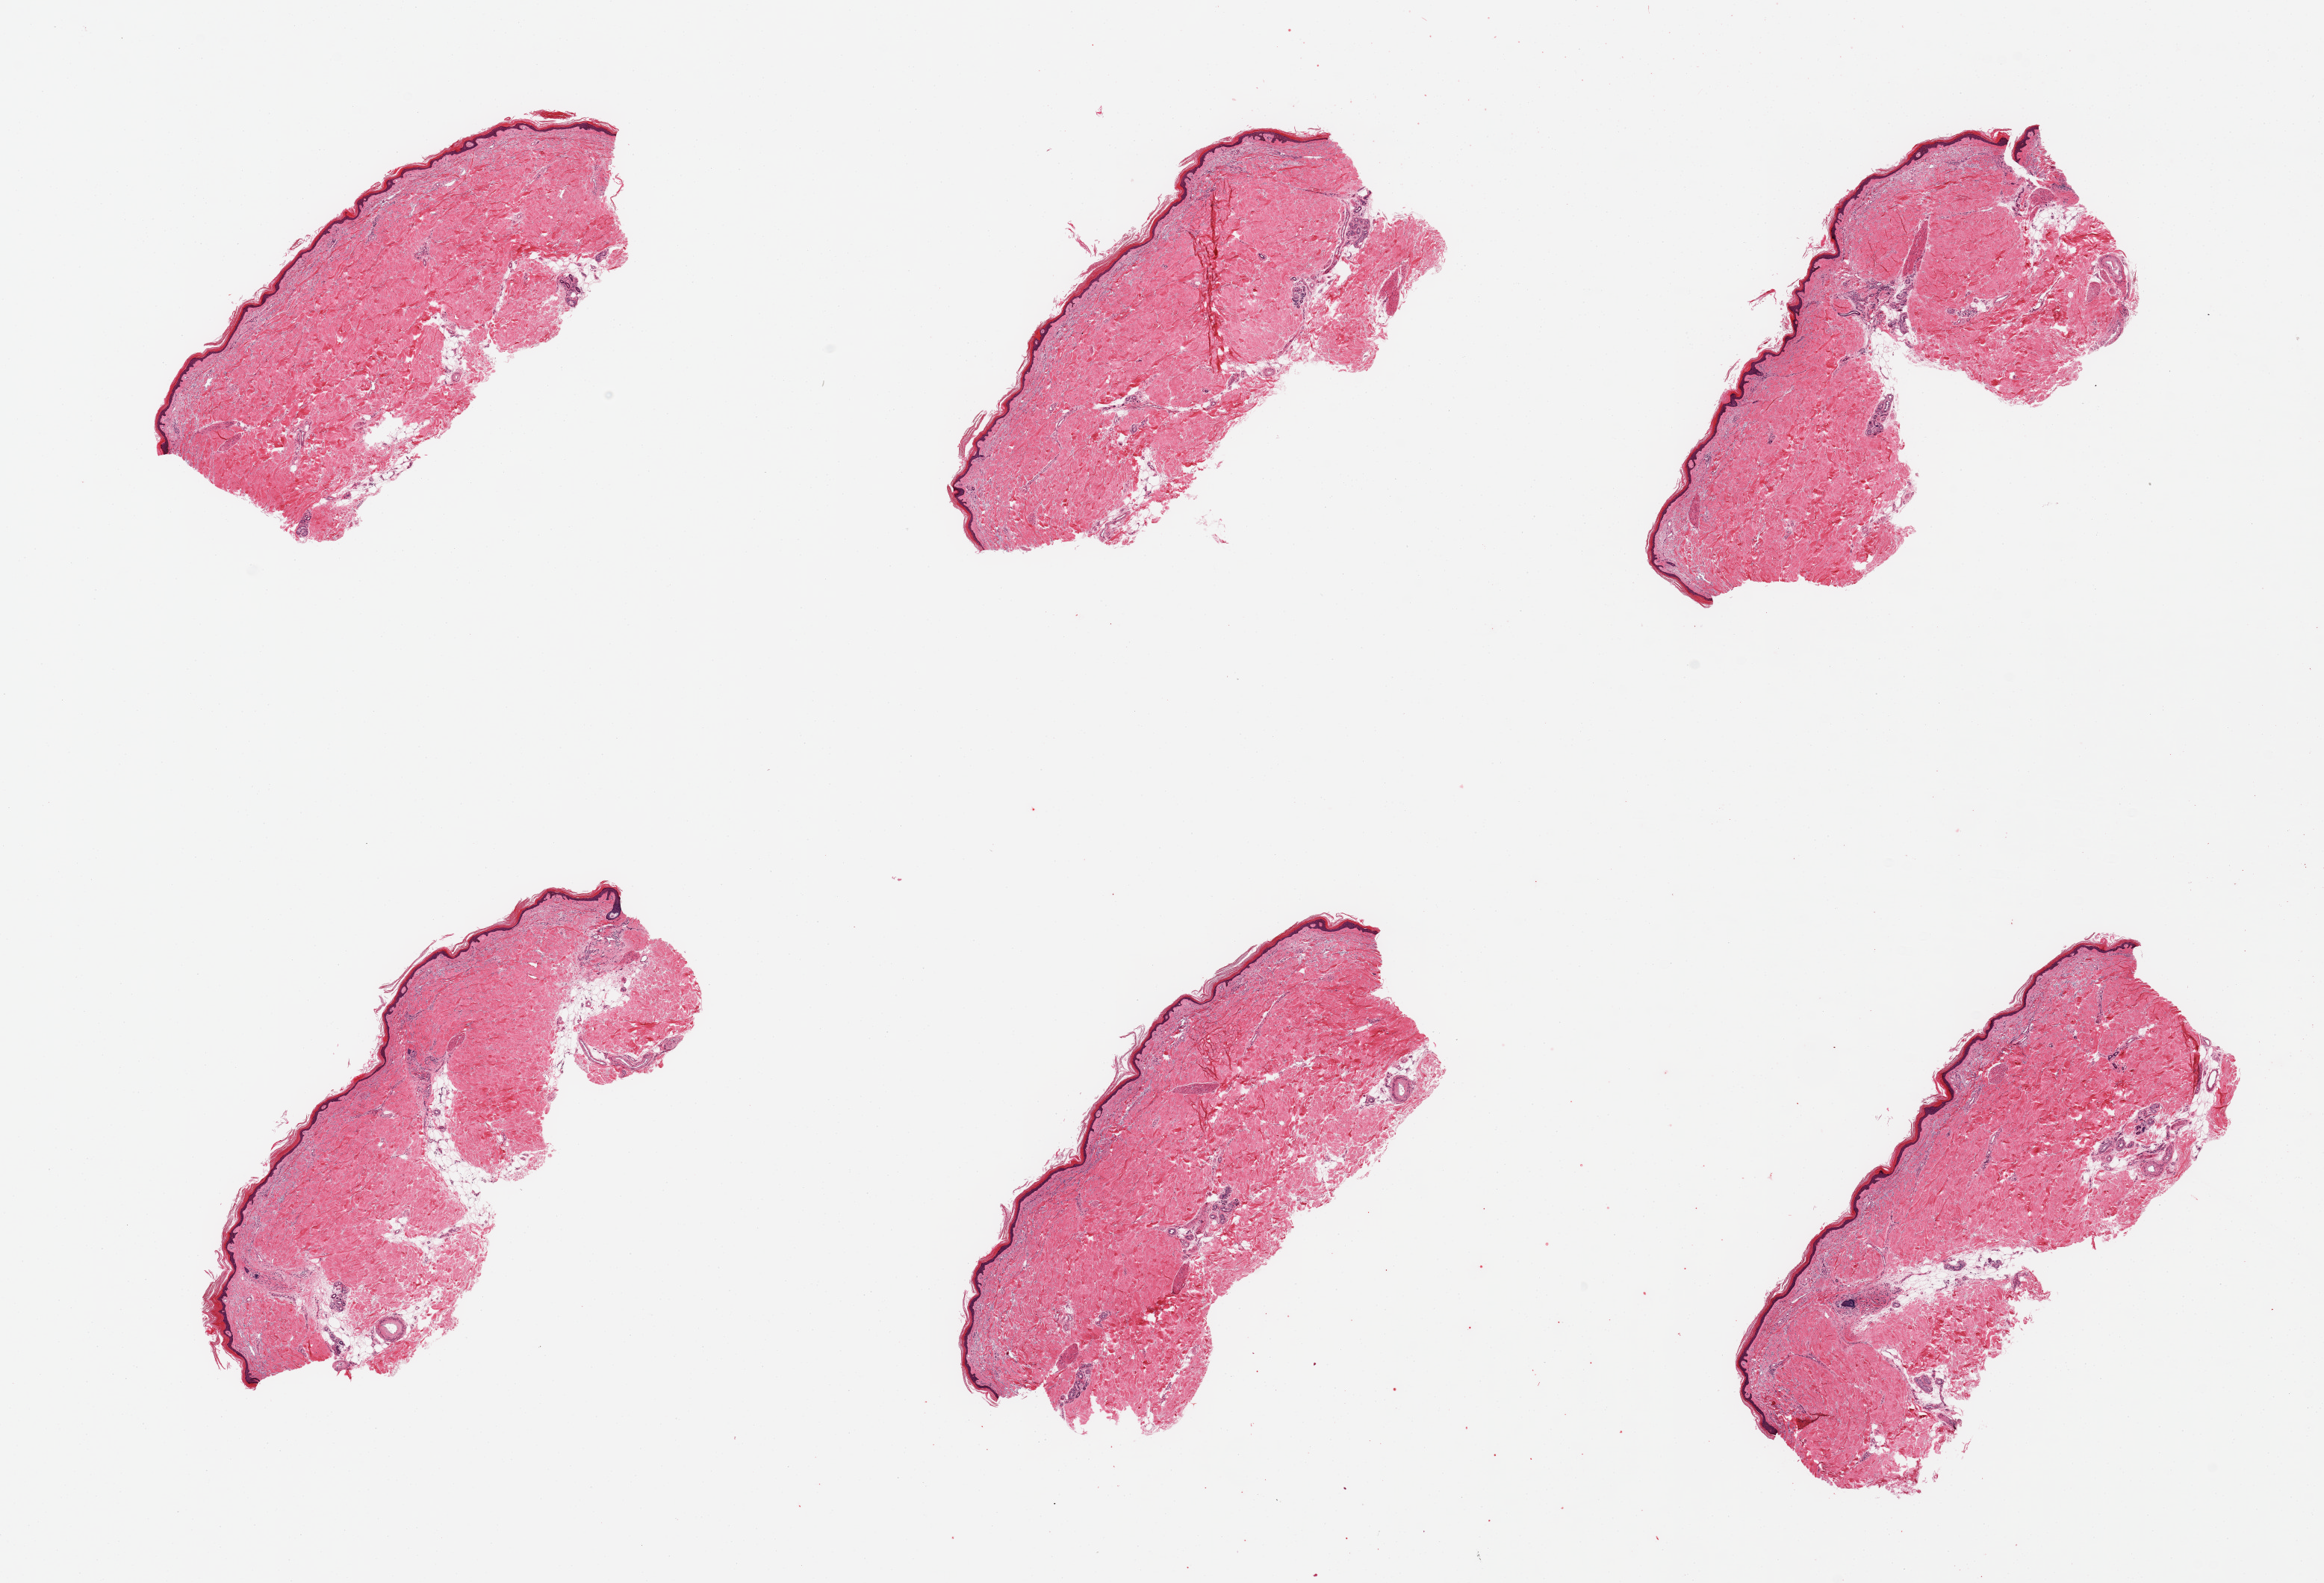
H&E whole-slide image, whole scanned area (about 24.6 x 16.8 mm) shown as a low-resolution overview, PAXgene-fixed paraffin-embedded (PFPE) section, target tissue: skin of lower leg, donor tissue sample. Donor: male.
- review note (as recorded): 6 pieces, minimal dermal fat; squamous eiptheliums is ~40-50 microns